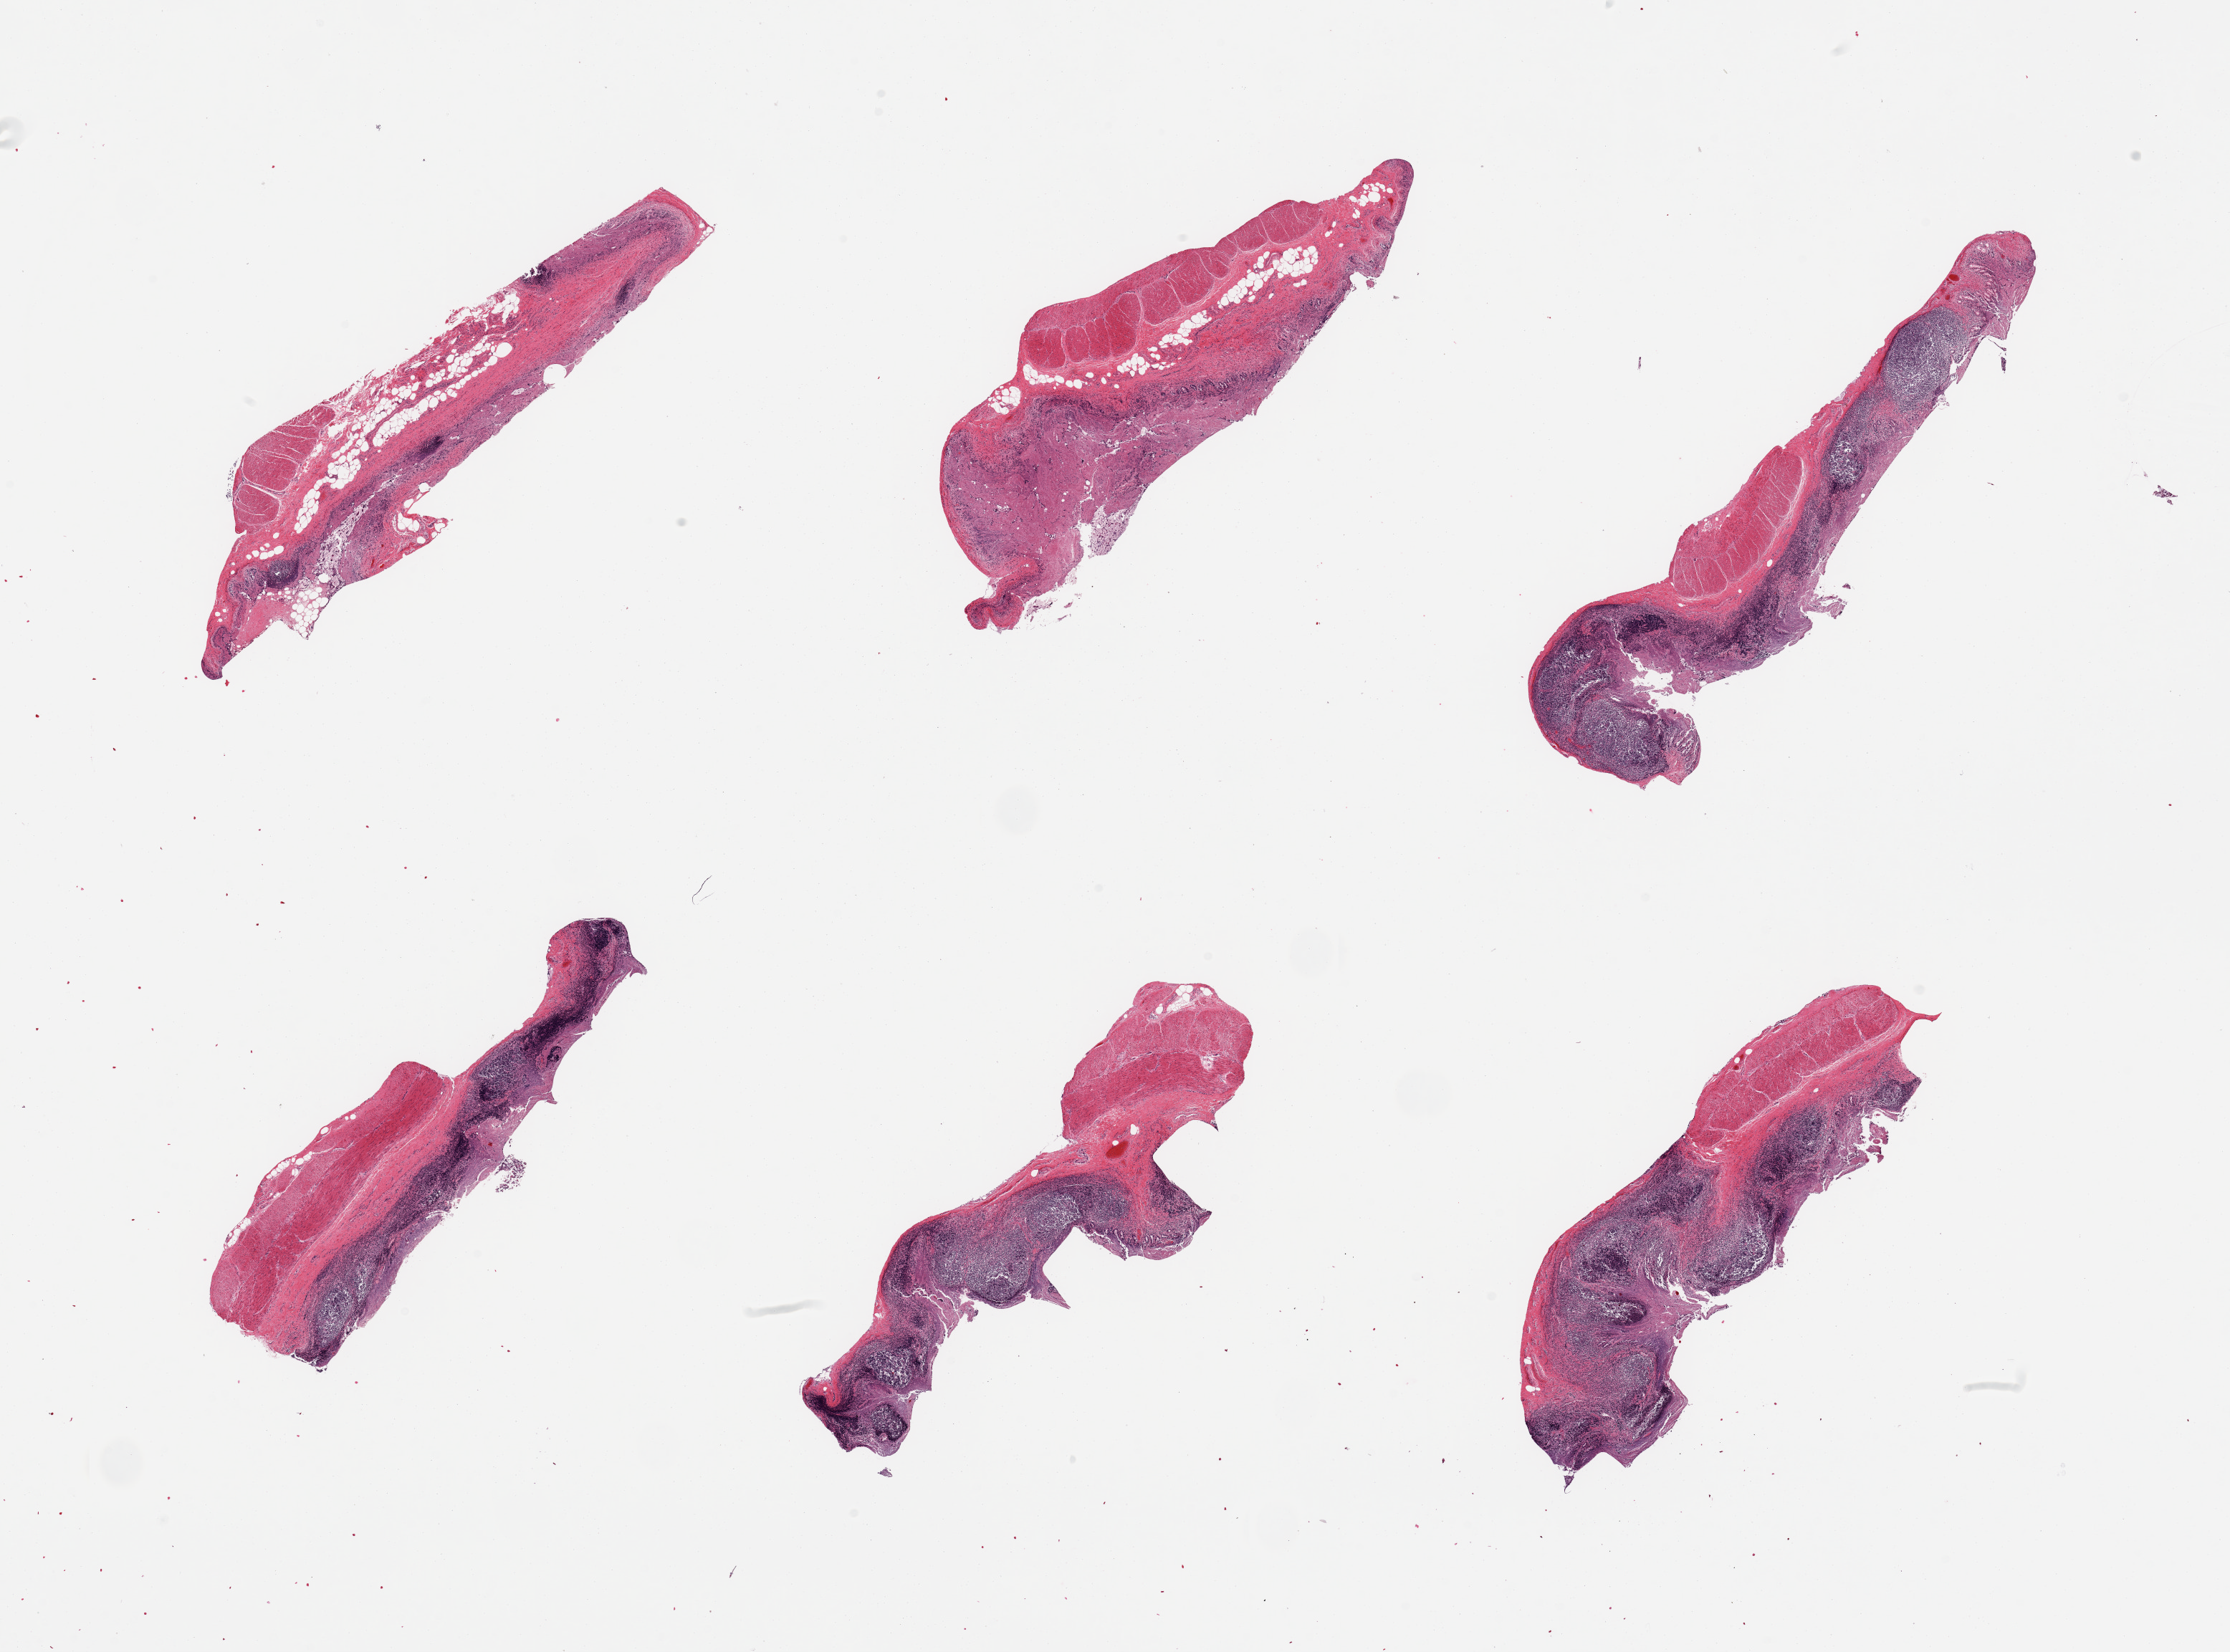
Whole-slide image, H&E stain — whole scanned area (about 24.6 x 18.2 mm, slide scanned at 20x) shown as a low-resolution overview; PAXgene-fixed paraffin-embedded (PFPE) section; target tissue: ileum; tissue donor sample. Donor: male.
Reviewer comment on this tissue sample: 6 pieces, glandular mucosa autolyzed; lymphoid aggregates are ~30% residual.